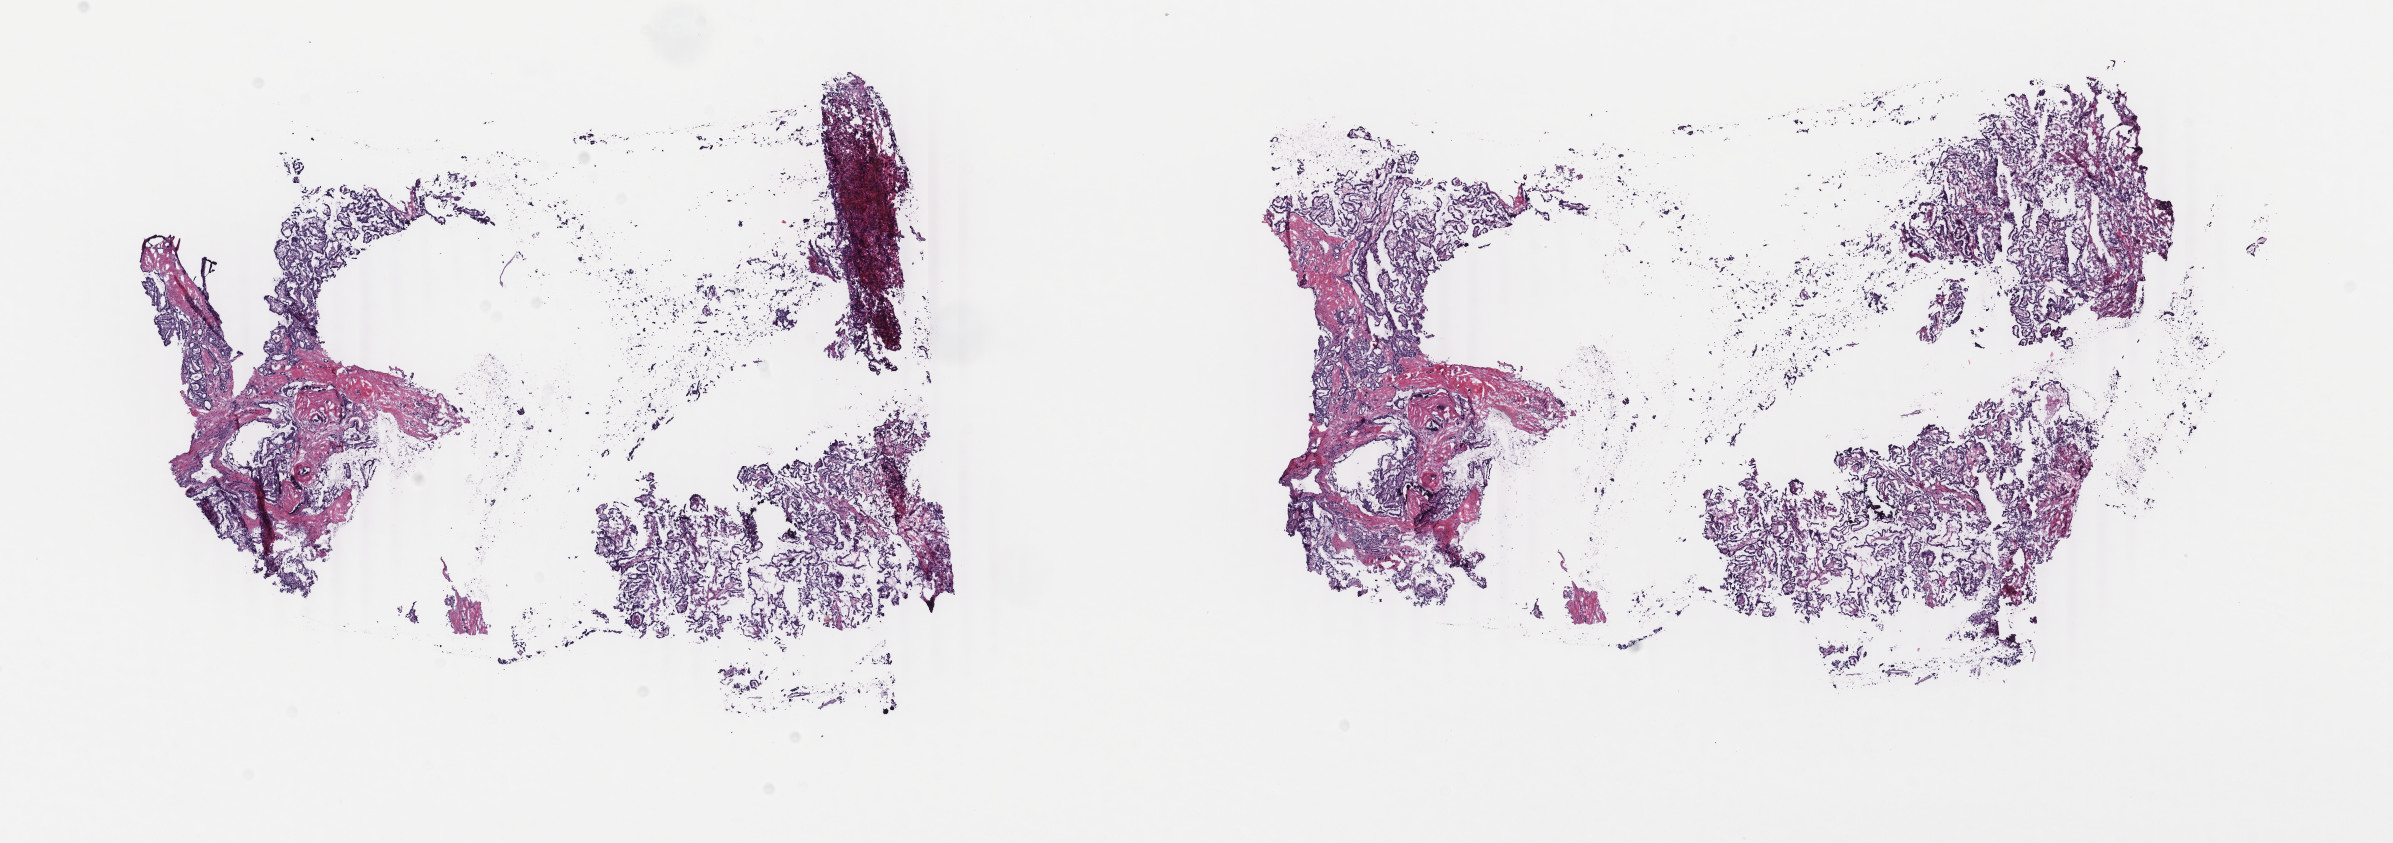
Digitized H&E tissue section (whole slide), shown as a low-resolution overview of the whole scanned area (about 19.0 x 6.7 mm, from a 40x scan), frozen section from the bottom of the tissue portion, thyroid, primary tumour sample. Female patient; age at initial diagnosis 21 years.
Diagnosis: Papillary adenocarcinoma, NOS.